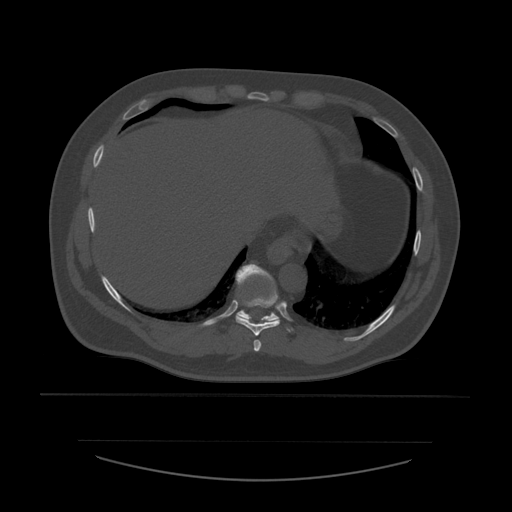
CT including the spine, one axial slice; slice 311 of 532 in the series (ordered by position); reconstruction kernel STANDARD; 120 kVp; bone window (W 1800 / L 400 HU); 512 × 512 image matrix. Patient age 44 years. From the clinical record (not read from this slice): primary cancer: soft tissue sarcoma.
Outlined on this slice (semi-automatically segmented with operator editing):
- T10 vertebra: bounding box <236,264,279,321> (left, top, right, bottom; pixels)
- T8 vertebra: <254,340,262,353>
- T9 vertebra: <236,279,281,336>